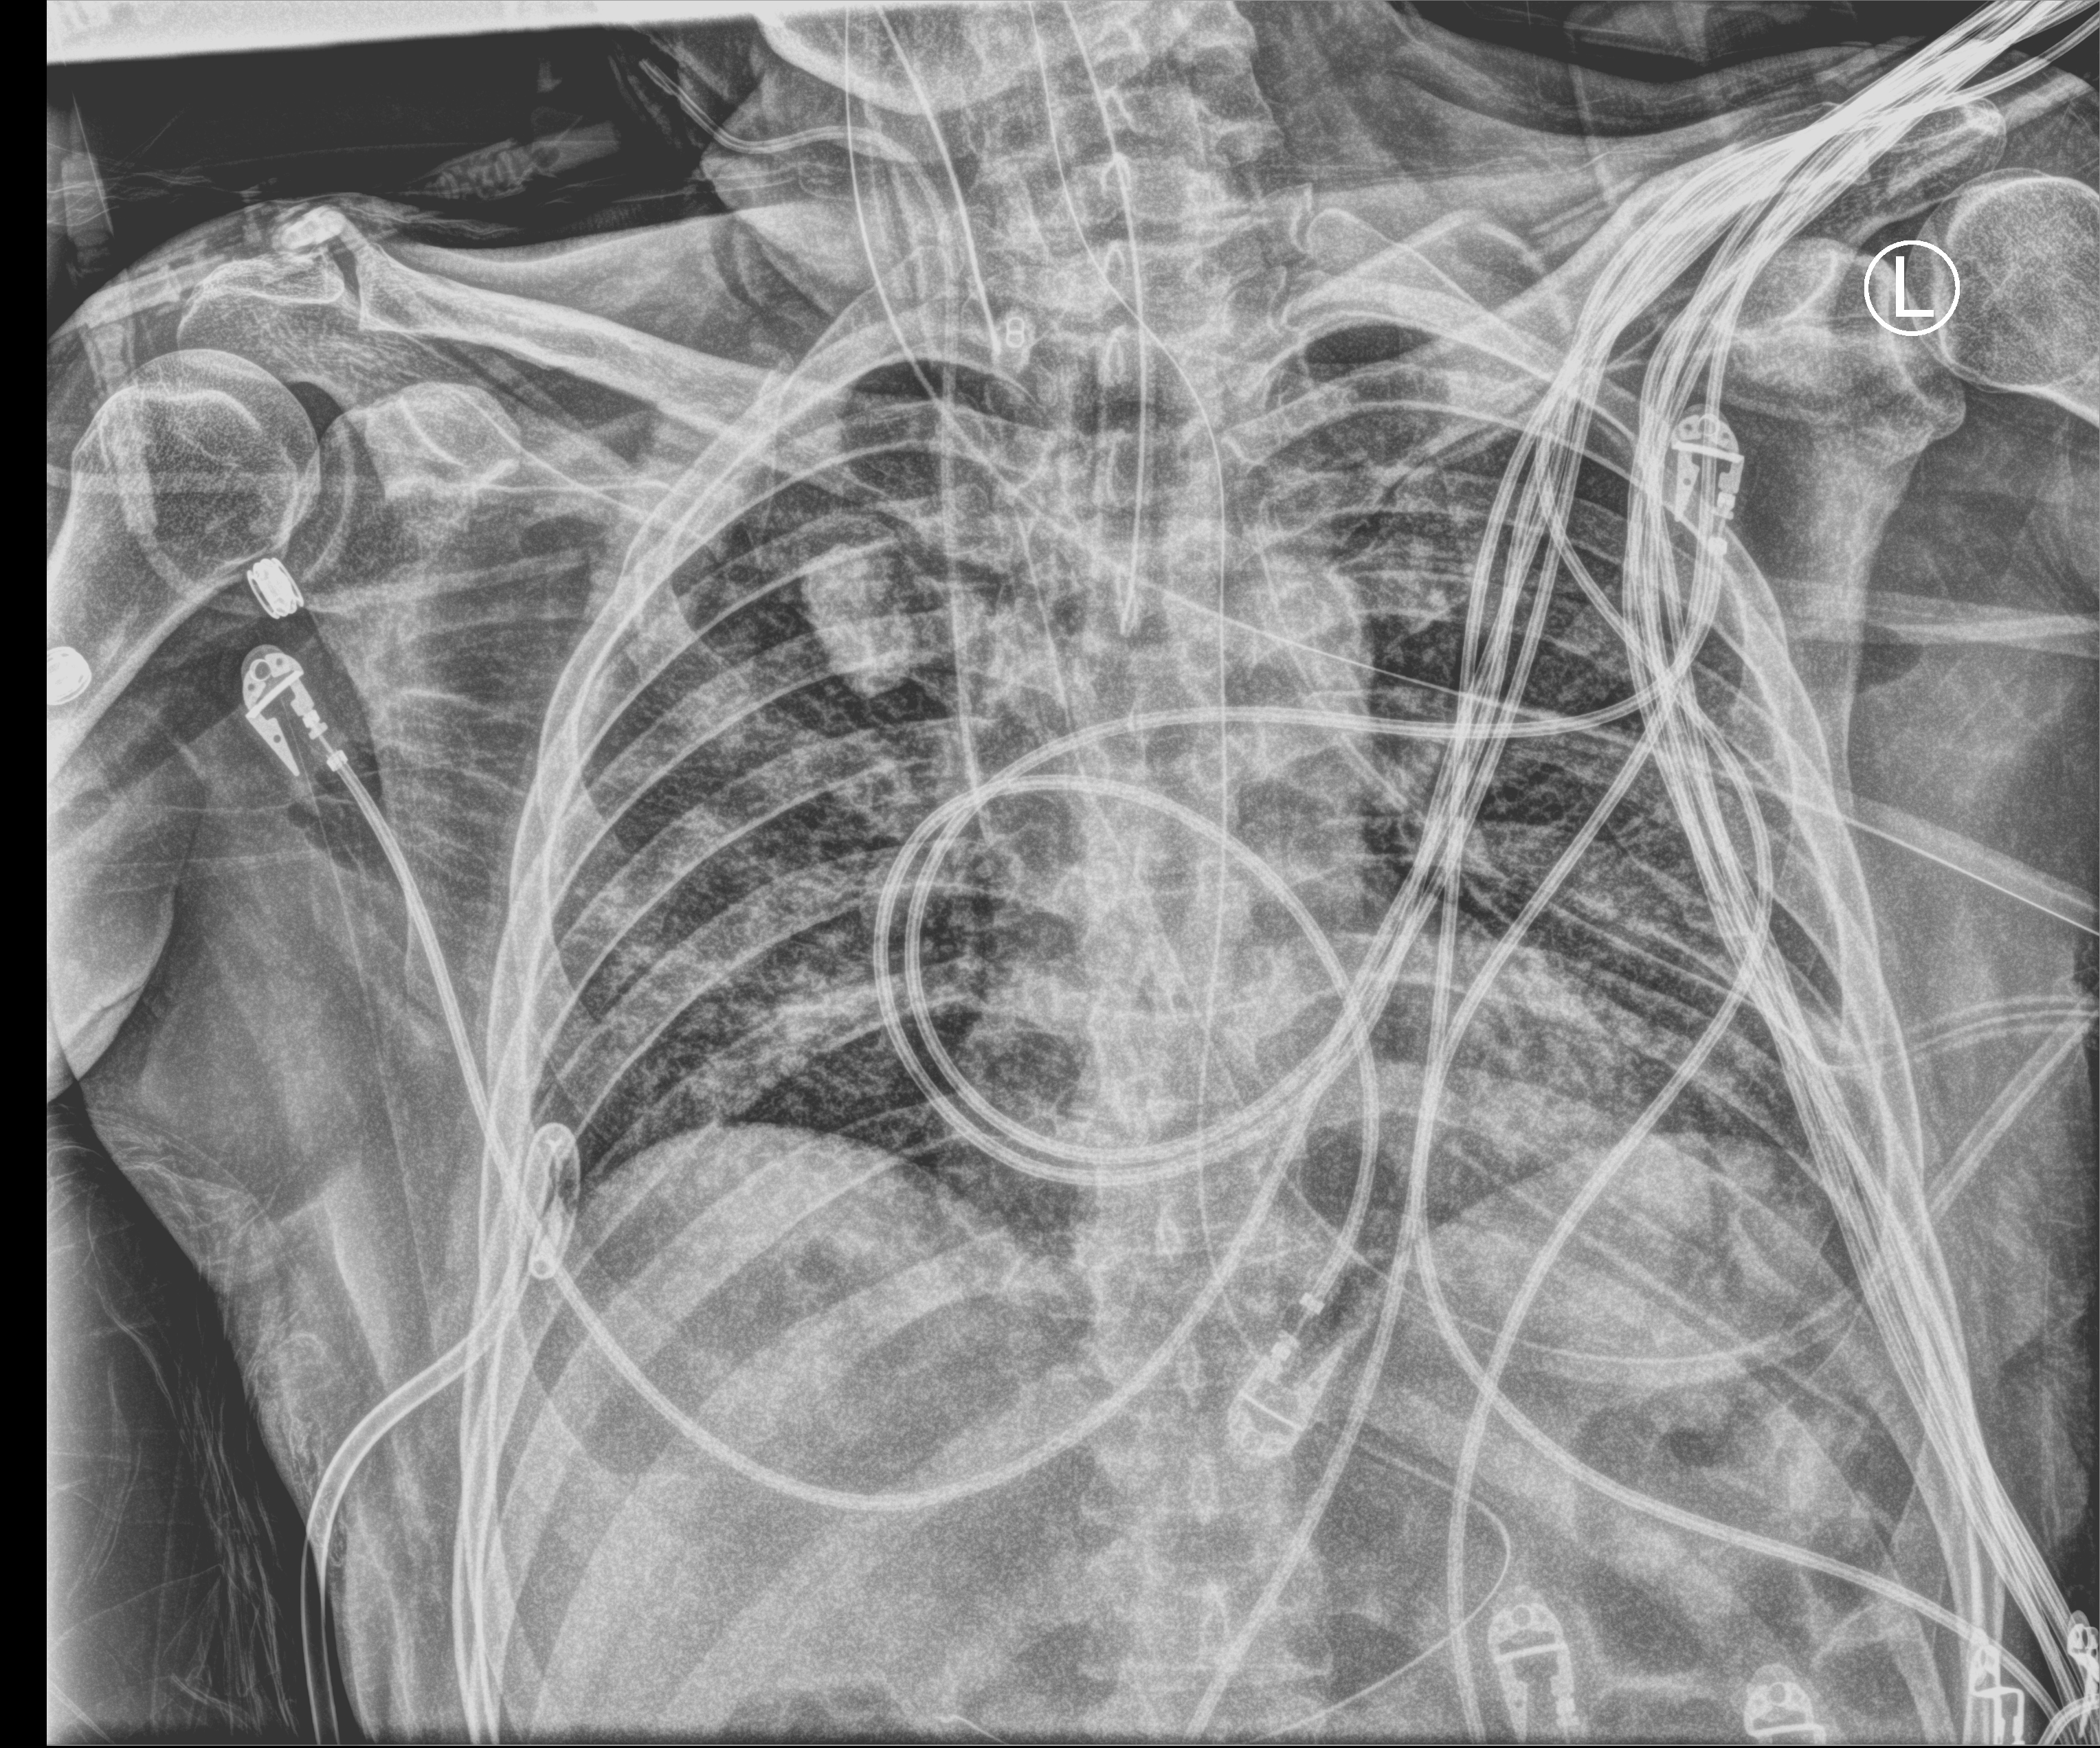
Portable chest radiograph. Patient hospitalised with COVID-19; male, aged 18–59 years.
From the hospital-stay record, not from the radiograph (when in the stay this image was taken is not recorded): admitted to intensive care during this hospital stay: yes.